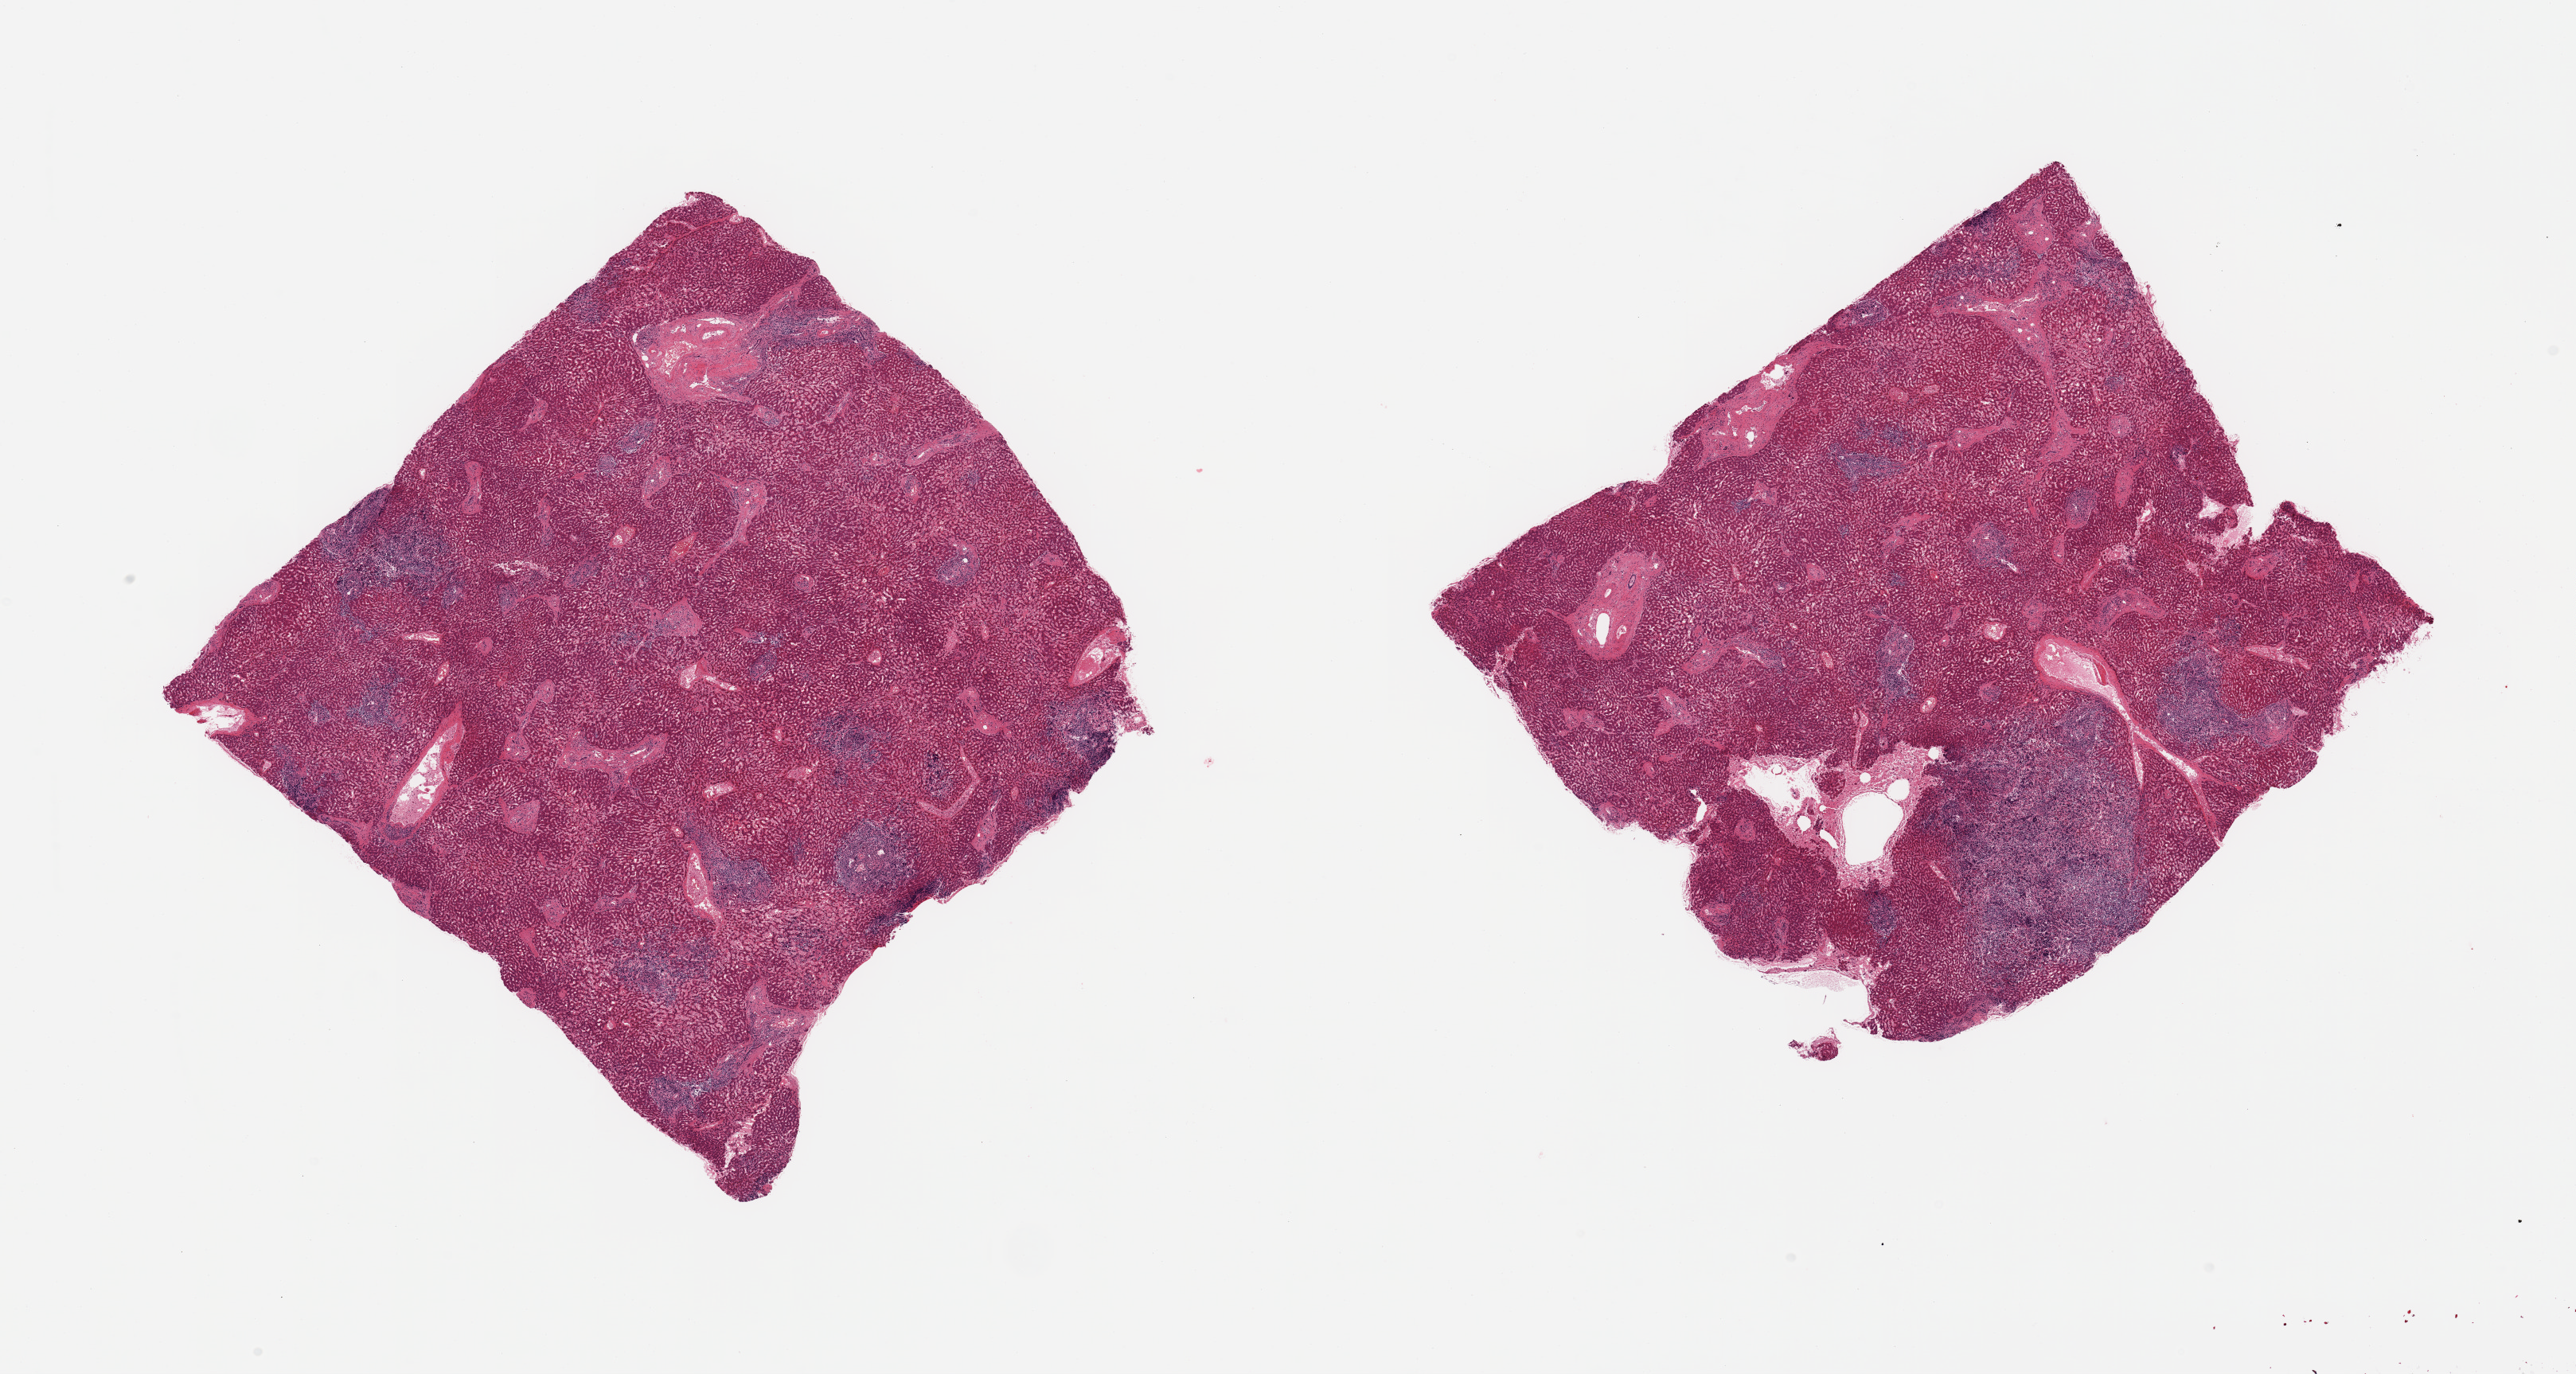
Digitized H&E-stained section — a low-resolution overview of the entire scanned area, about 25.6 x 13.7 mm; PAXgene-fixed paraffin-embedded (PFPE) section; target tissue: liver; donor tissue sample. Donor sex: male.
* reviewer comment on this tissue sample: 2 pieces; atypical lymphoid infiltrates